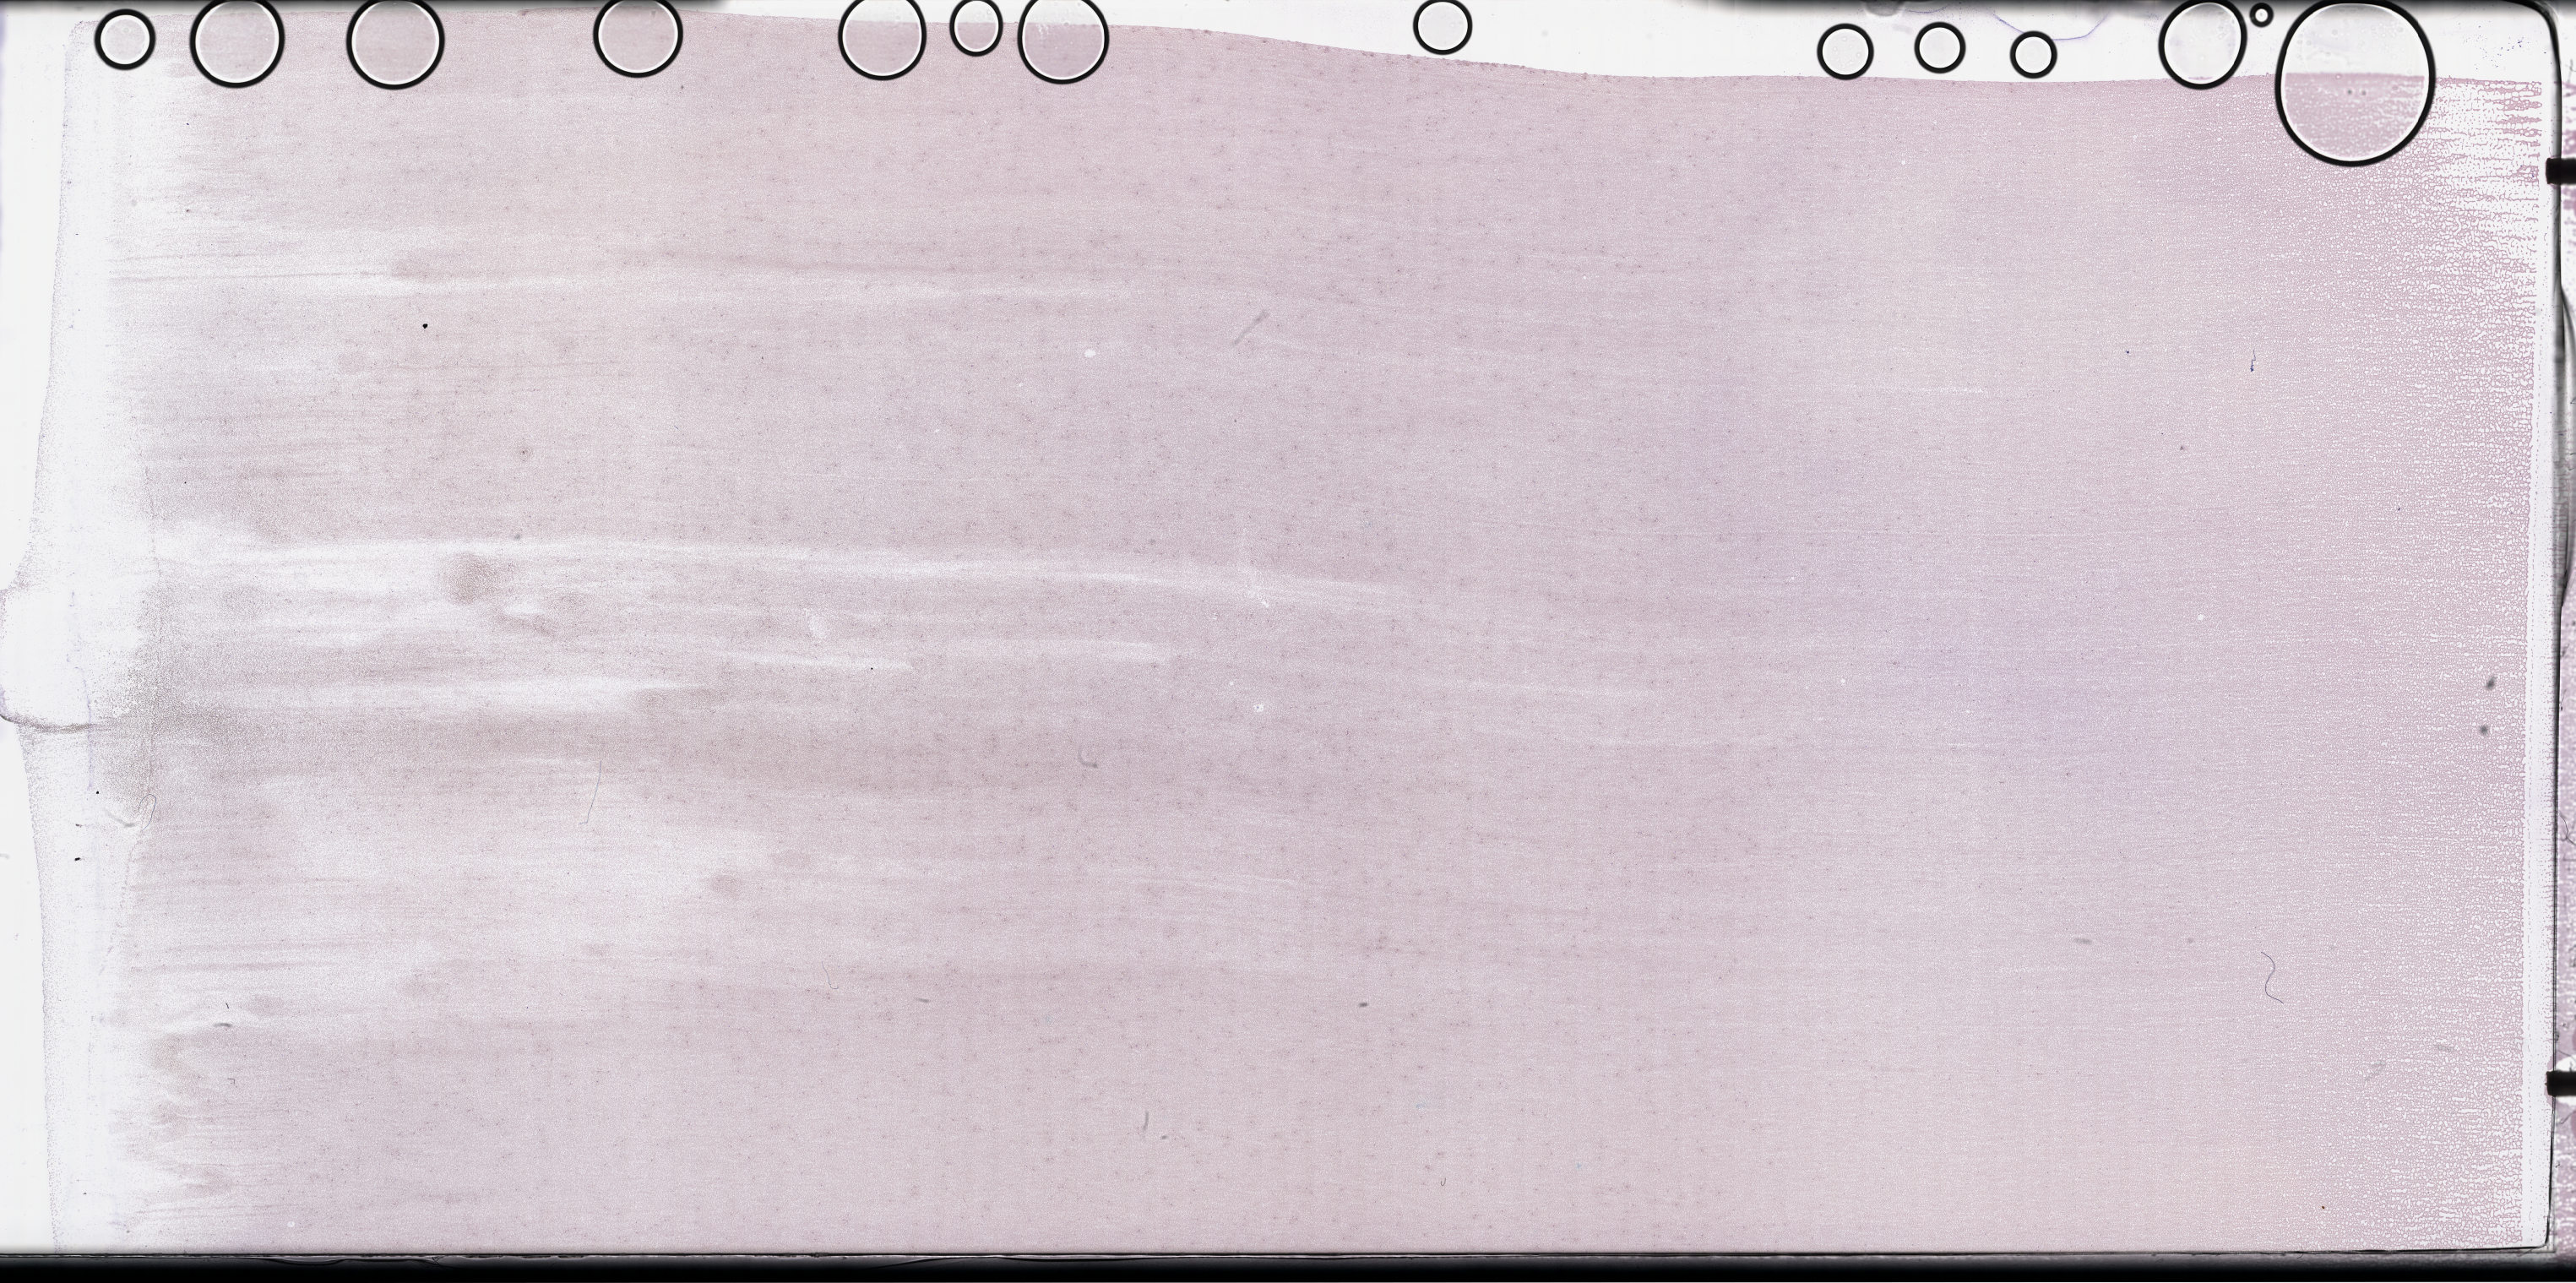
Whole-slide image of a whole blood smear, Wright-Giemsa stain, whole scanned area (about 49.3 x 24.5 mm) shown as a low-resolution overview. Specimen time point: collected on treatment. Patient sex: female.
• from a patient with: Plasma Cell Myeloma